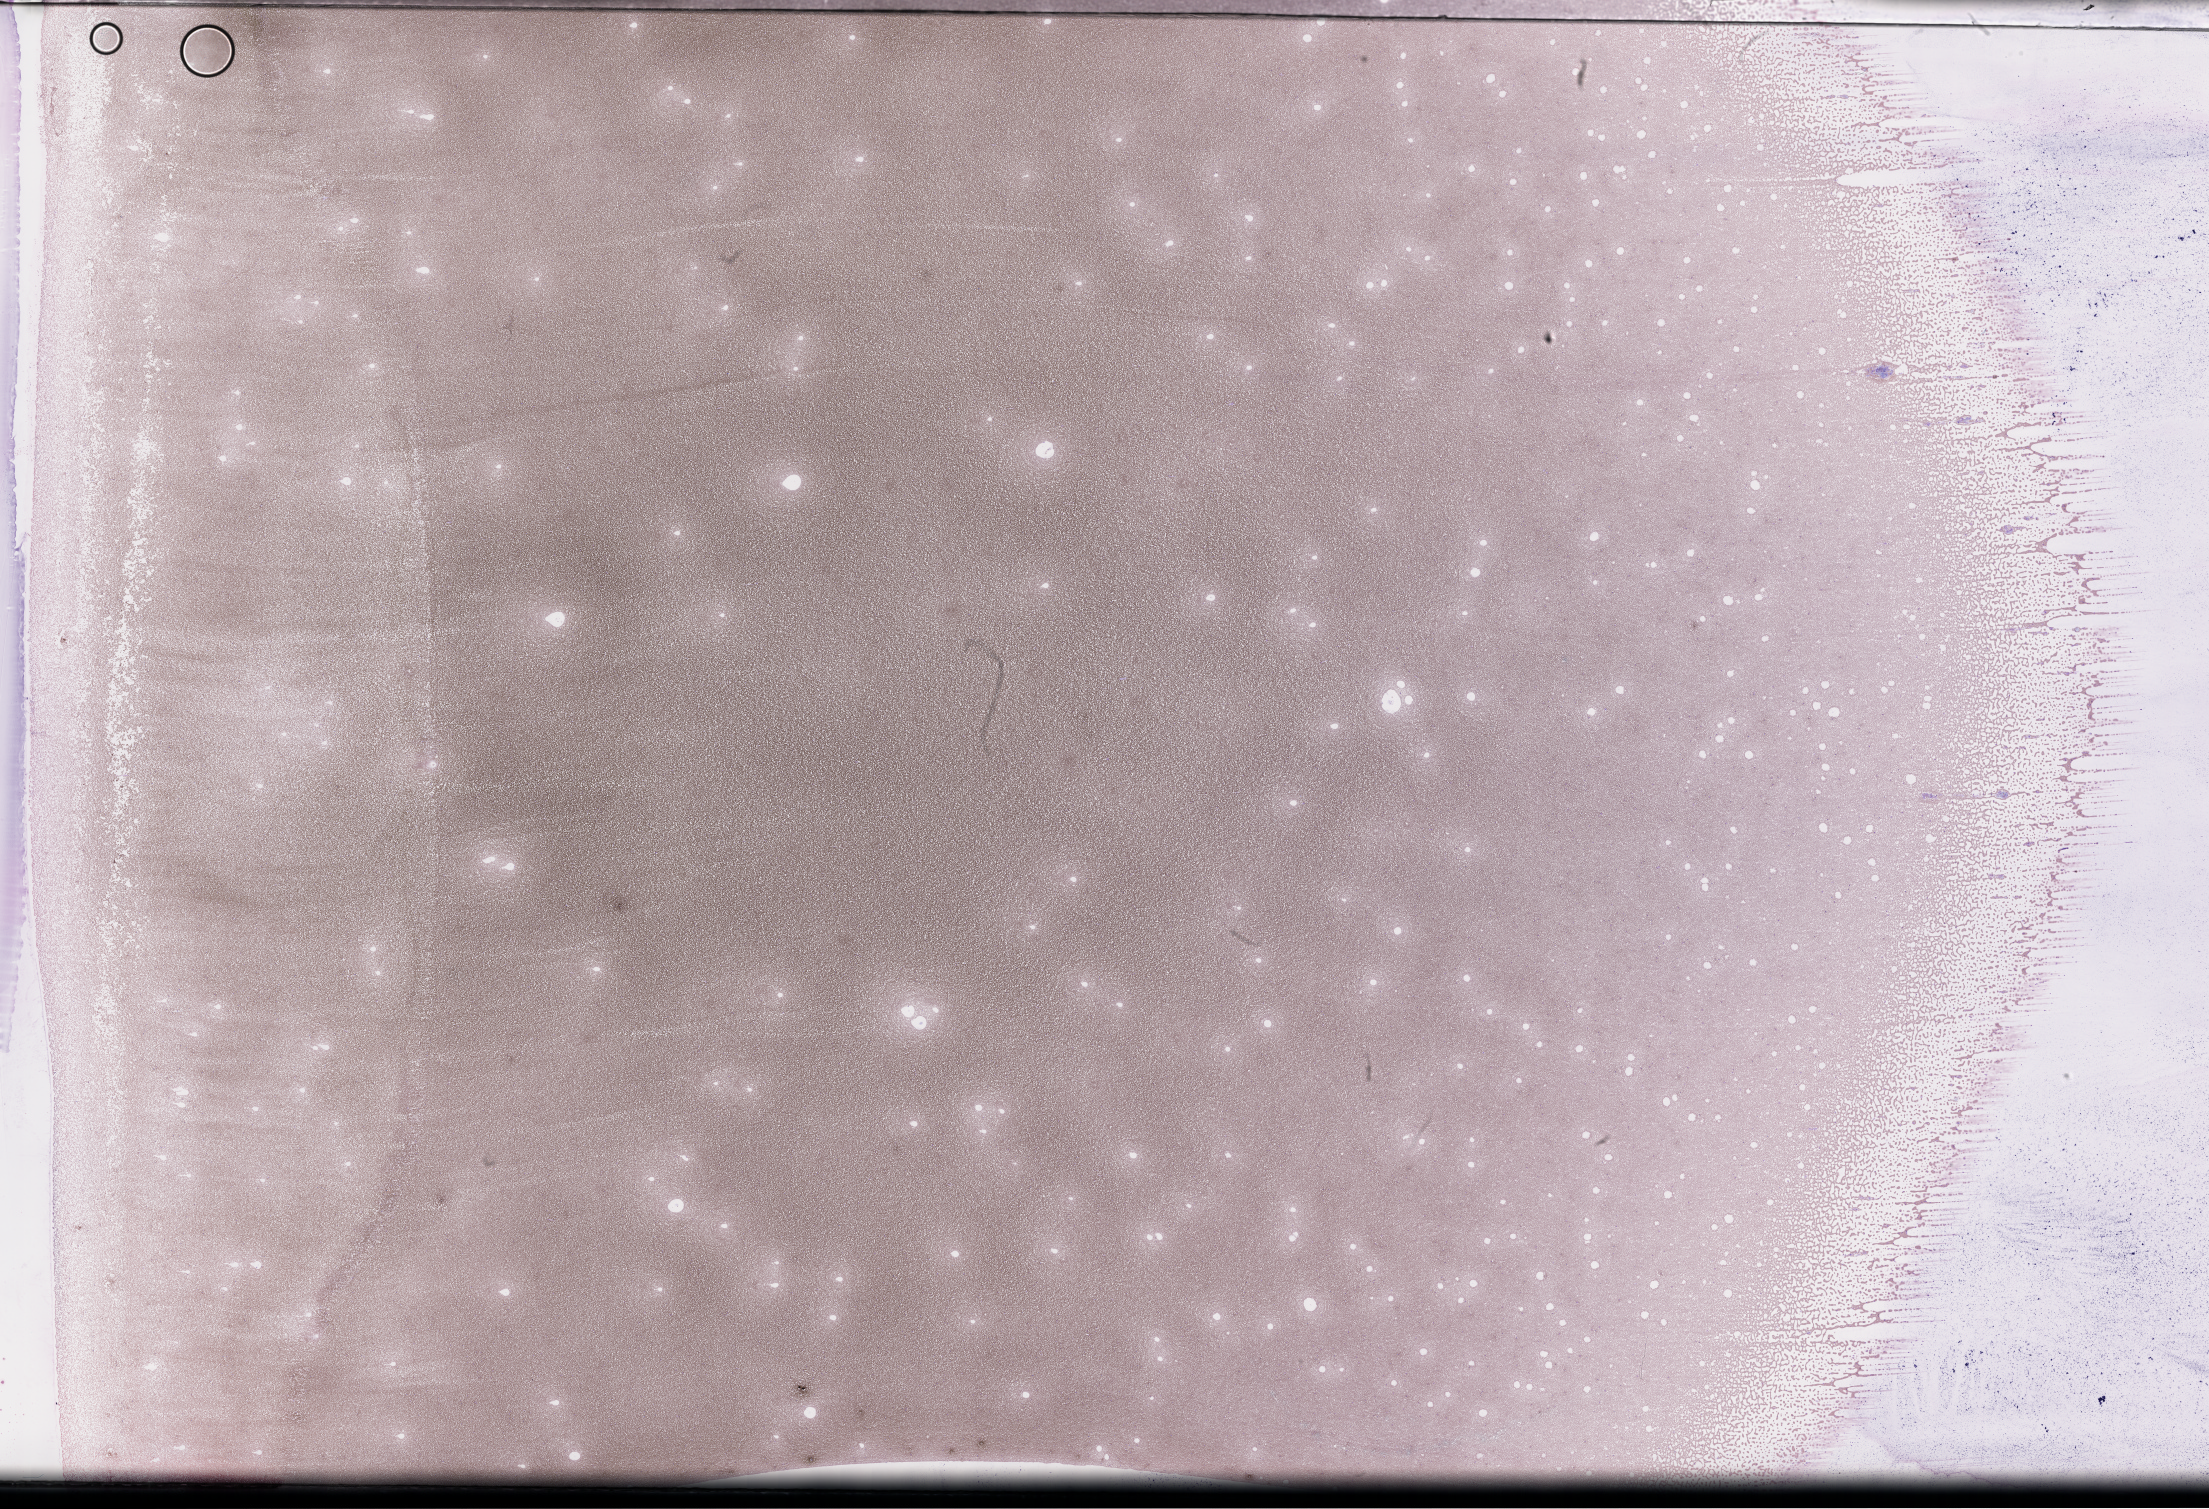
Whole-slide image of a whole blood smear, Wright–Giemsa stain — low-resolution overview of the scanned area, about 35.7 x 24.4 mm; smear from an EDTA sample; specimen time point: collected on treatment. Patient sex: male.
Patient diagnosis: Plasma Cell Myeloma.